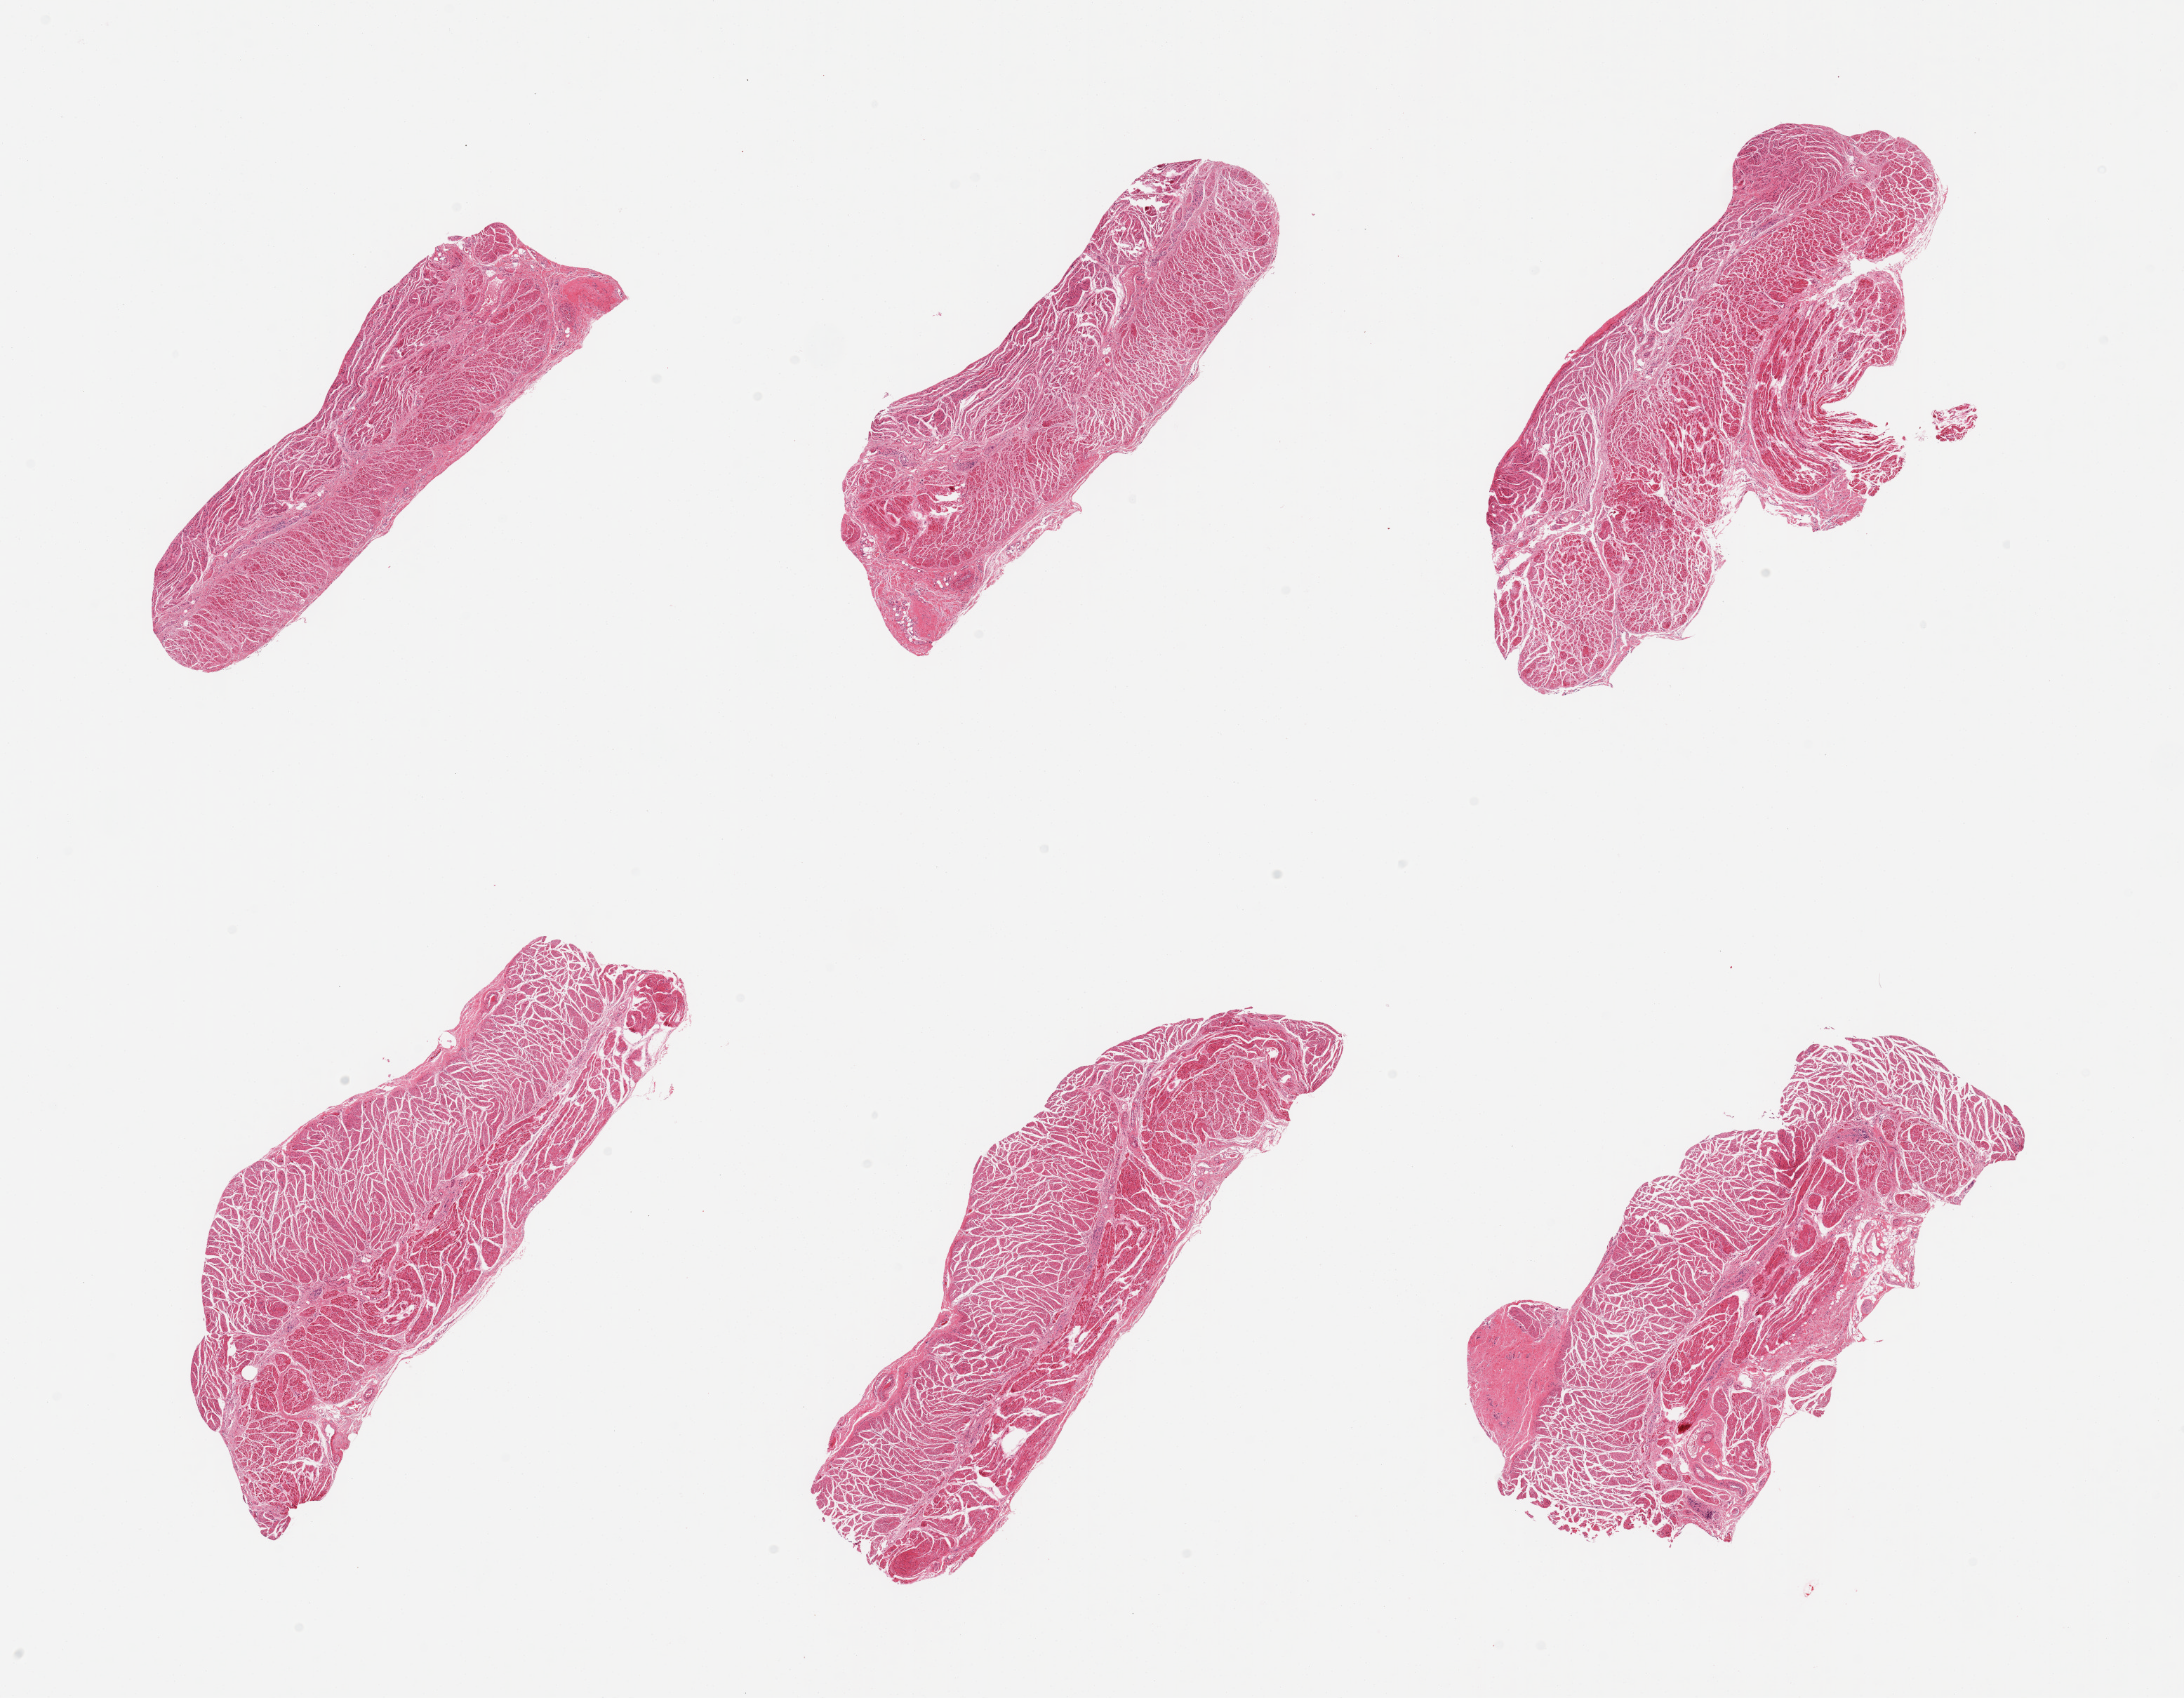
Digitized haematoxylin and eosin-stained section, brightfield — shown as a low-resolution overview of the whole scanned area (about 24.6 x 19.1 mm); PAXgene-fixed, paraffin-embedded tissue; target tissue: gastroesophageal junction; donor tissue sample. Female donor.
Reviewer comment on this tissue sample: 6 pieces, all muscularis.